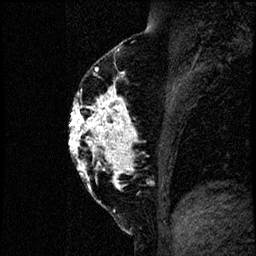
Breast MRI (dynamic contrast-enhanced), one sagittal slice. Slice 36 of 60 in the series (ordered by position). Dynamic contrast-enhanced study with each time point stored as its own series, time point 2 of 4 at this slice position (early post-contrast, ordered by acquisition time). 1.5 T. TE 4.2 ms, TR 17.6 ms. 2 mm slice thickness. 256 × 256 image matrix, field of view 200 × 200 mm. Patient: female, 40 years. From the clinical record (not read from this slice): setting: breast cancer imaged before/during neoadjuvant chemotherapy; receptor status: HER2-positive.
Annotated regions visible in this slice (semi-automatically segmented with operator editing):
- analysis volume of interest (the breast-tissue region the enhancement analysis was run in; not a lesion): box from (x=66, y=55) to (x=185, y=206) px
- tumour enhancement mask (voxels above the 100 % enhancement threshold inside the analysis volume of interest): (x=68, y=69)–(x=134, y=181)